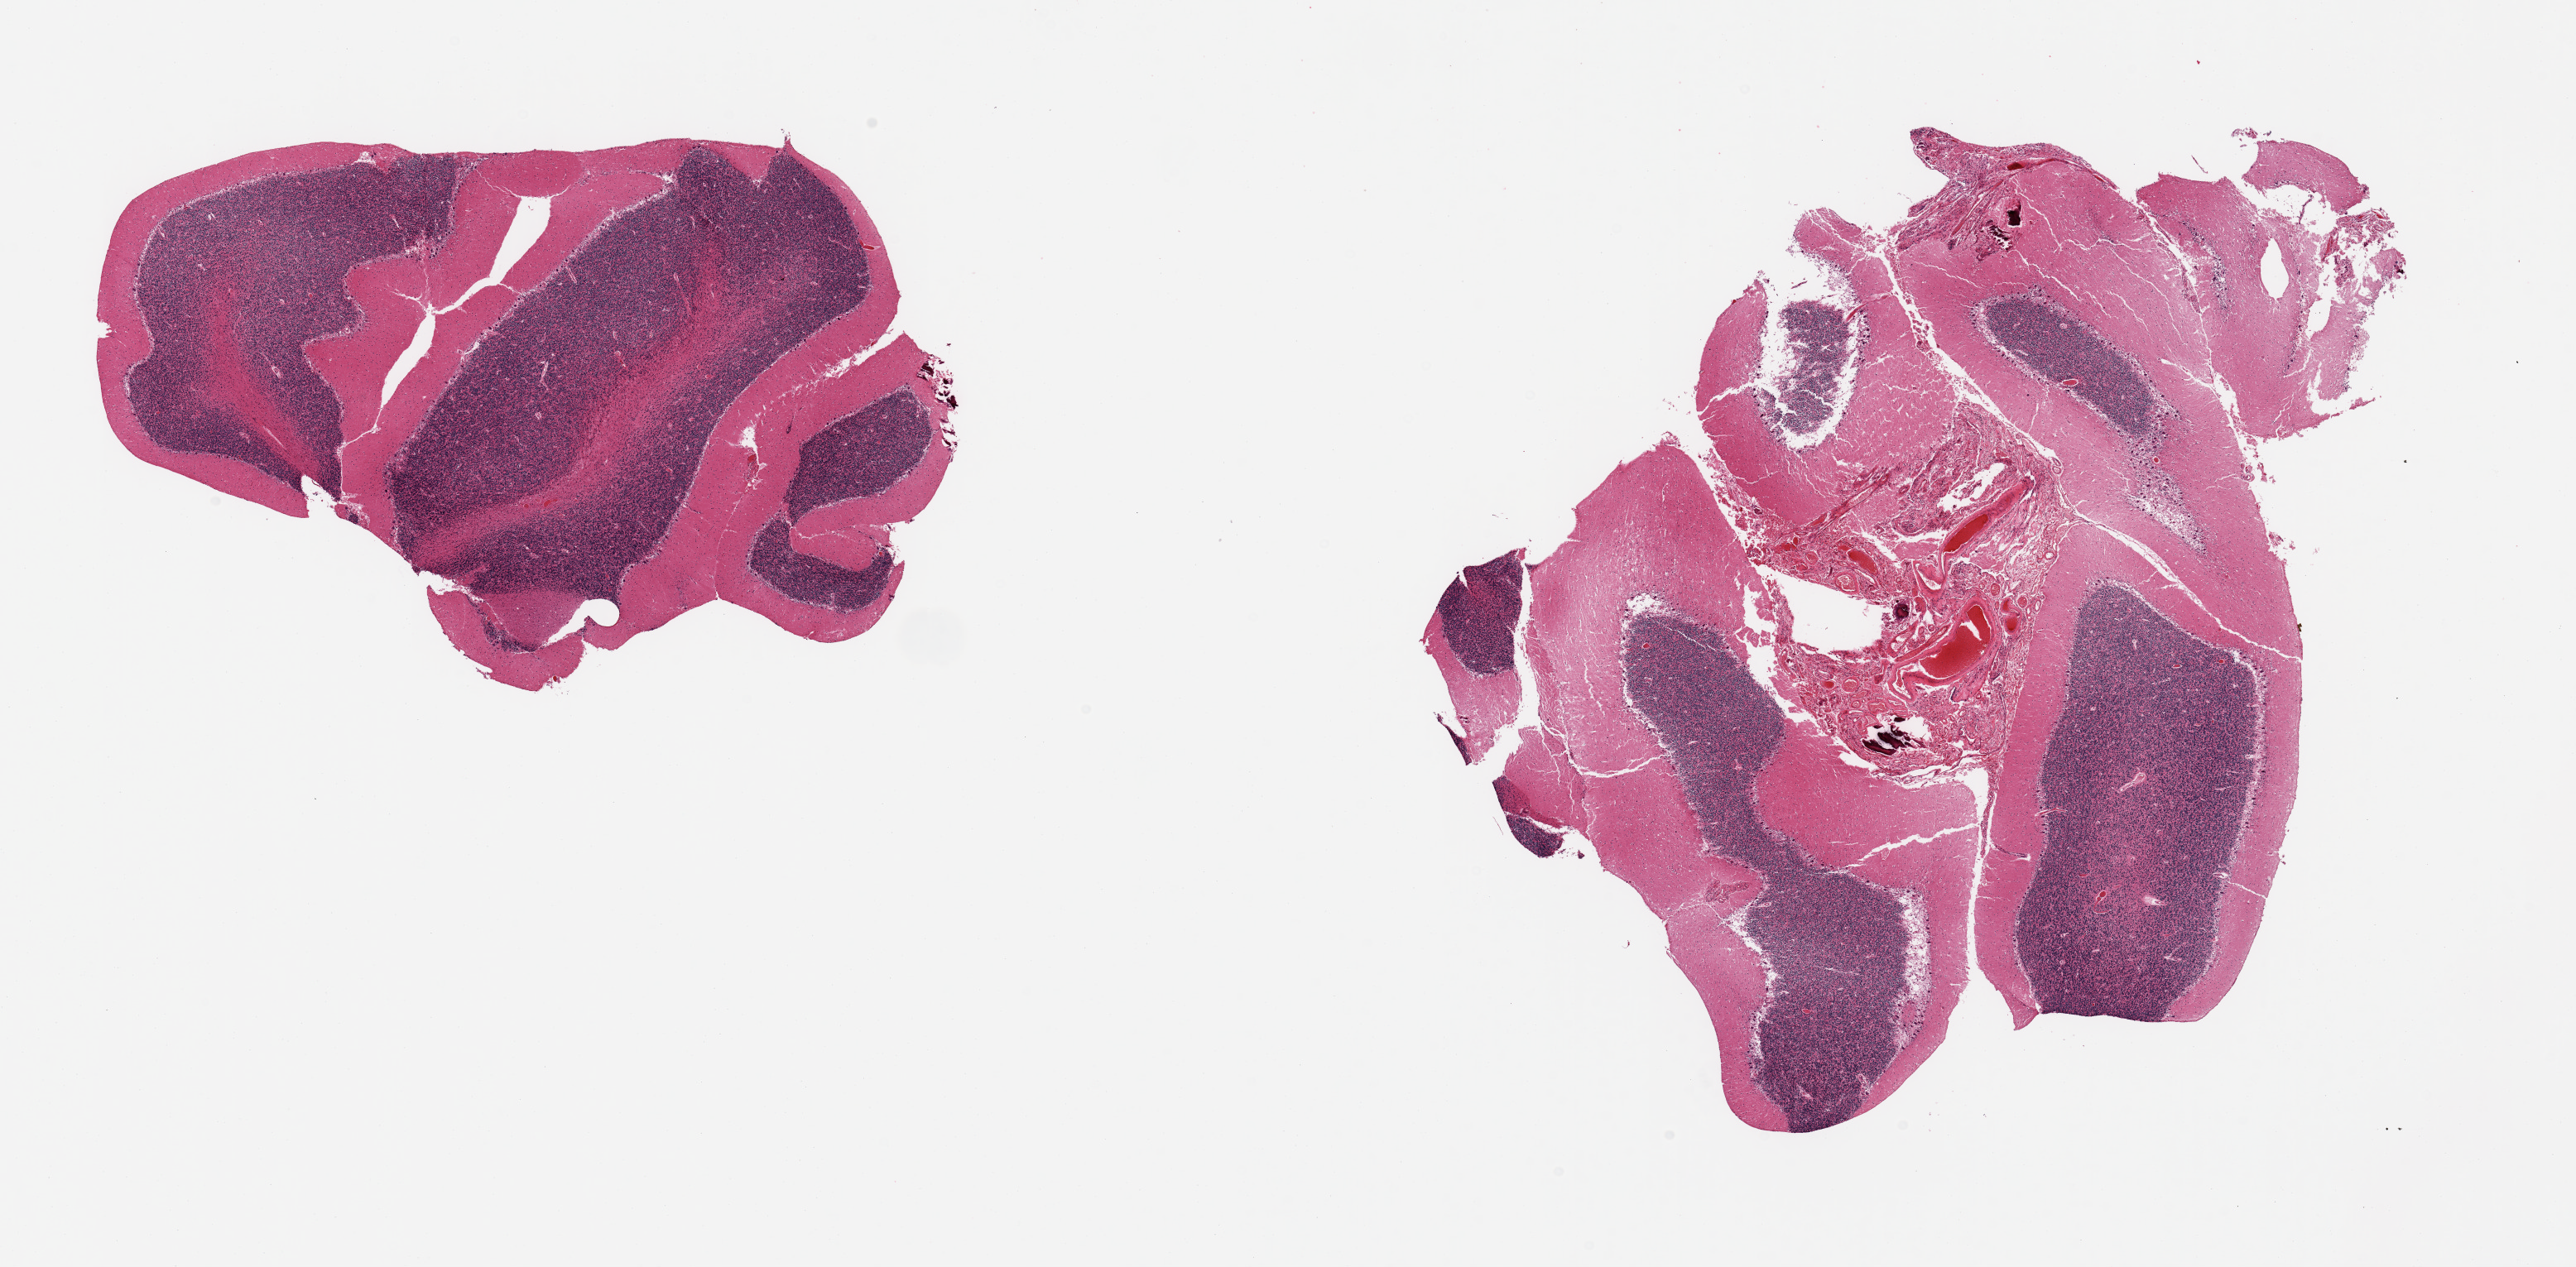
Whole-slide image, hematoxylin and eosin (H&E) stain, brightfield — whole scanned area (about 24.6 x 12.1 mm, from a 20x scan) shown as a low-resolution overview; PAXgene-fixed paraffin-embedded (PFPE) section; target tissue: cerebellum; tissue donor sample. Donor sex: male.
- reviewer comment on this tissue sample: 2 pieces; Purkinje cells are well visualized, 1 piece includes portion of meninges